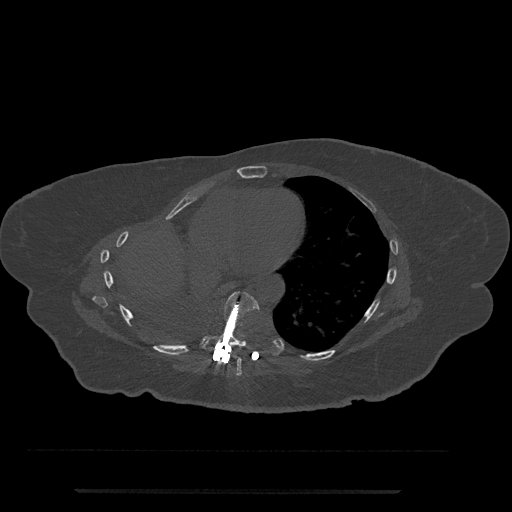
CT including the spine, one axial slice; slice 400 of 797 in the series (ordered by position); reconstruction kernel Br40s/3; bone window (W 1800 / L 400 HU); 0.5 mm slice thickness; 512 × 512 image matrix, field of view 440 × 440 mm. Female patient, age 51 years. Case-level facts recorded for this patient, not image findings: primary cancer: neuro; vertebrae with lytic lesions (as recorded): T8.
Annotated regions visible in this slice (semi-automatic segmentation, software-assisted and operator-edited):
- T7 vertebra: bounding box <233,359,242,376> (left, top, right, bottom; pixels)
- T8 vertebra: <202,291,260,352>